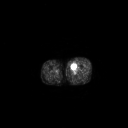
FDG PET of an extremity soft-tissue mass (from a PET/CT study), one axial slice. 3.27 mm slice thickness. 128 × 128 image matrix. Patient: male, 48 years. Case-level facts recorded for this patient, not image findings: histological type: pleiomorphic leiomyosarcoma; grade: high; site of the primary tumour: left thigh.
Outlined on this slice (expert contour drawn on MRI and transferred to this co-registered scan by the dataset authors):
- gross tumour volume including surrounding oedema: bounding box <69,62,77,71> (left, top, right, bottom; pixels)
- gross tumour volume (mass): <70,64,76,71>